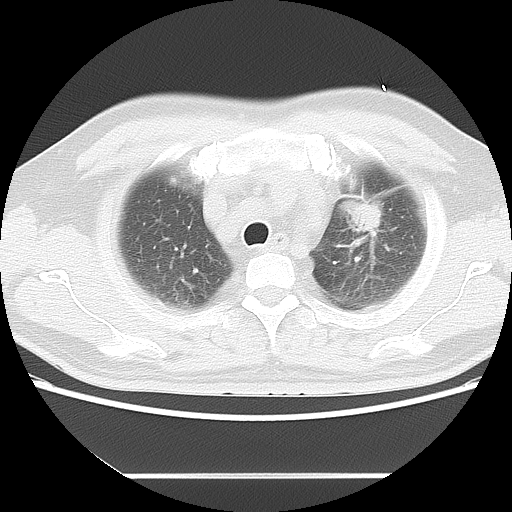
Chest CT, one axial slice; slice 10 of 14 in the series (ordered by position); 120 kVp; lung window (W 1500 / L -600 HU); 5 mm slice thickness; 512 × 512 image matrix. Patient: male, 56 years. Case-level facts recorded for this patient, not image findings: clinical TNM (as recorded): T2 N3 M1.
Annotated regions visible in this slice (bounding box drawn by a radiologist):
- lung tumour (recorded histology: adenocarcinoma): box from (x=343, y=191) to (x=389, y=239) px